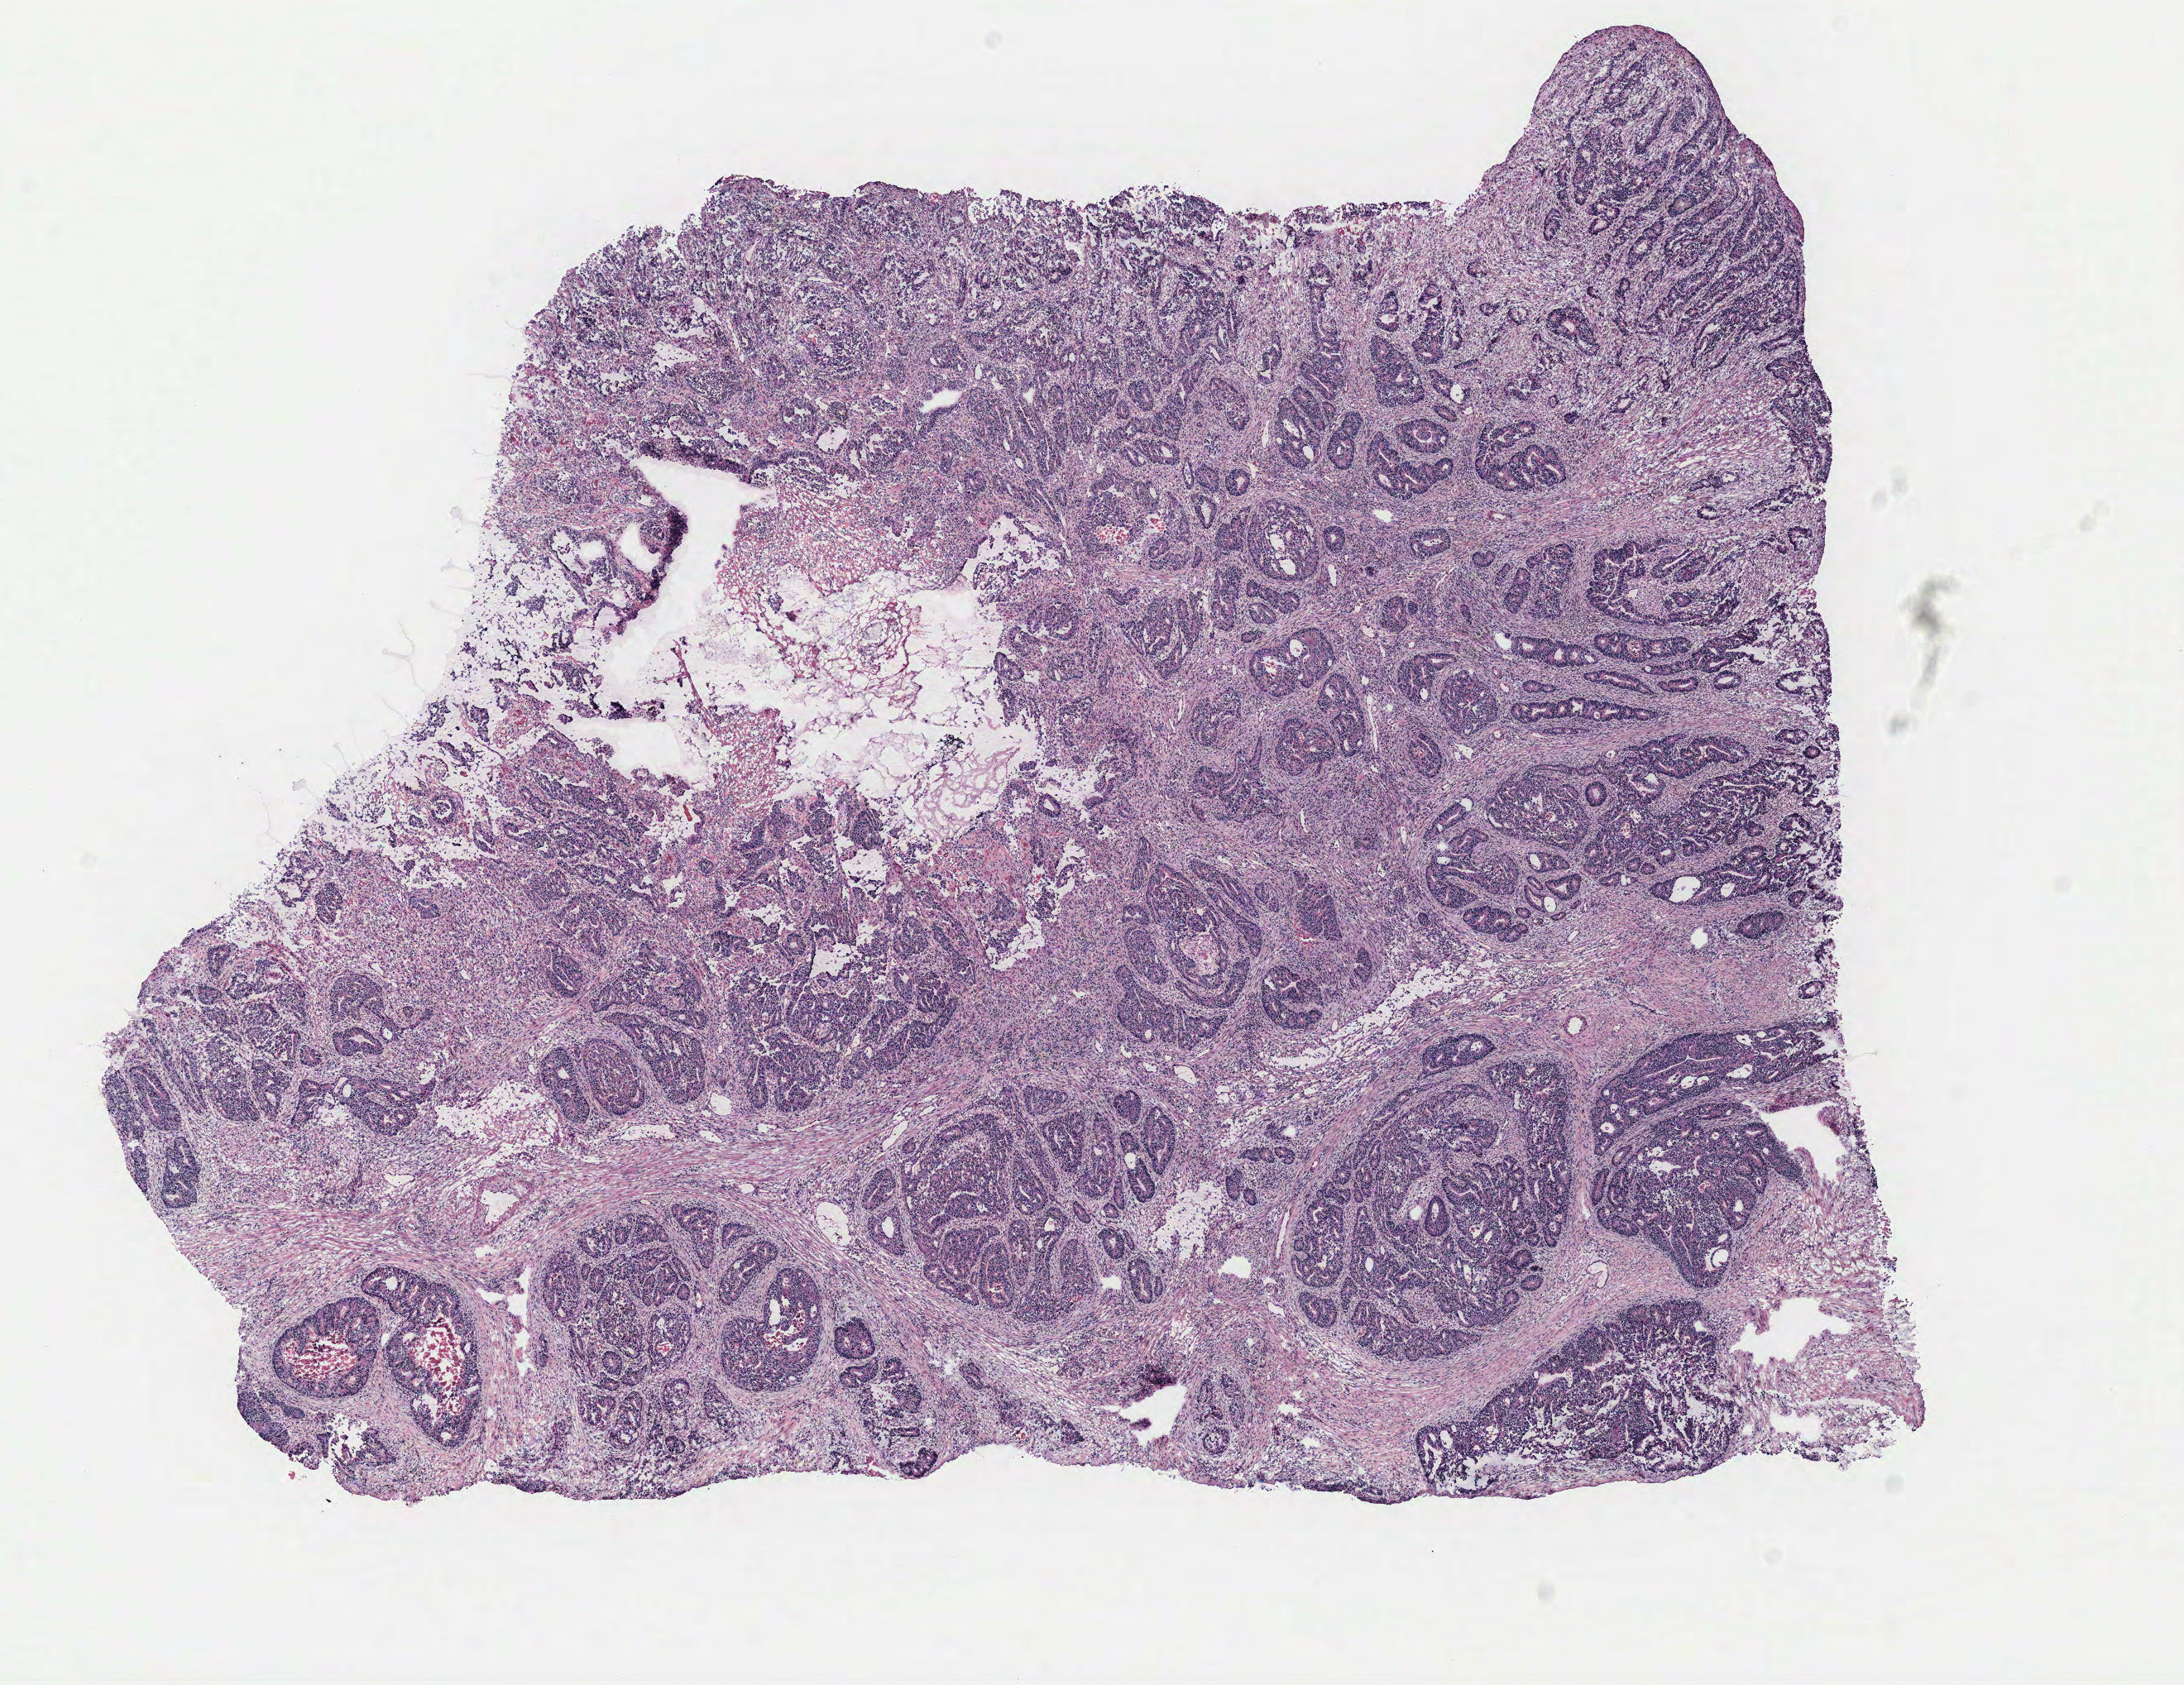
H&E whole-slide image — whole scanned area (about 10.6 x 8.2 mm, slide scanned at 40x) shown as a low-resolution overview. Tumour tissue sample, colon. Patient: female, age 40 years.
Primary tumour site (as recorded): colon. Patient diagnosis (cohort enrolment): colon cancer (colon).